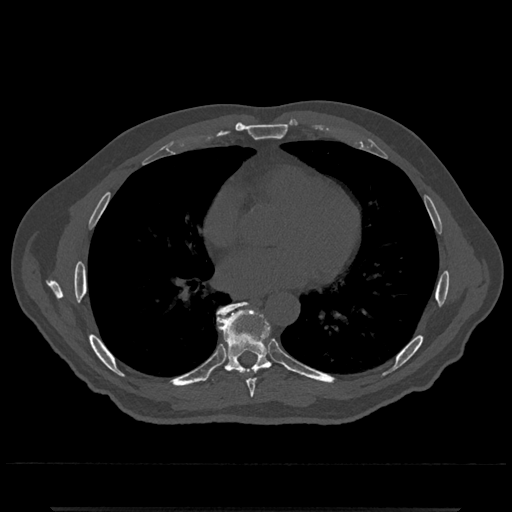
CT including the spine, one axial slice; position 690 of 797 along the scan axis; reconstruction kernel Br40s/3; 120 kVp; bone window (W 1800 / L 400 HU); 0.5 mm slice thickness; 512 × 512 image matrix, field of view 393 × 393 mm. Male patient, age 67 years. Case-level facts recorded for this patient, not image findings: primary cancer: prostate.
Outlined on this slice (semi-automatic segmentation, software-assisted and operator-edited):
- T7 vertebra: bounding box <247,368,265,398> (left, top, right, bottom; pixels)
- T8 vertebra: <208,302,272,384>